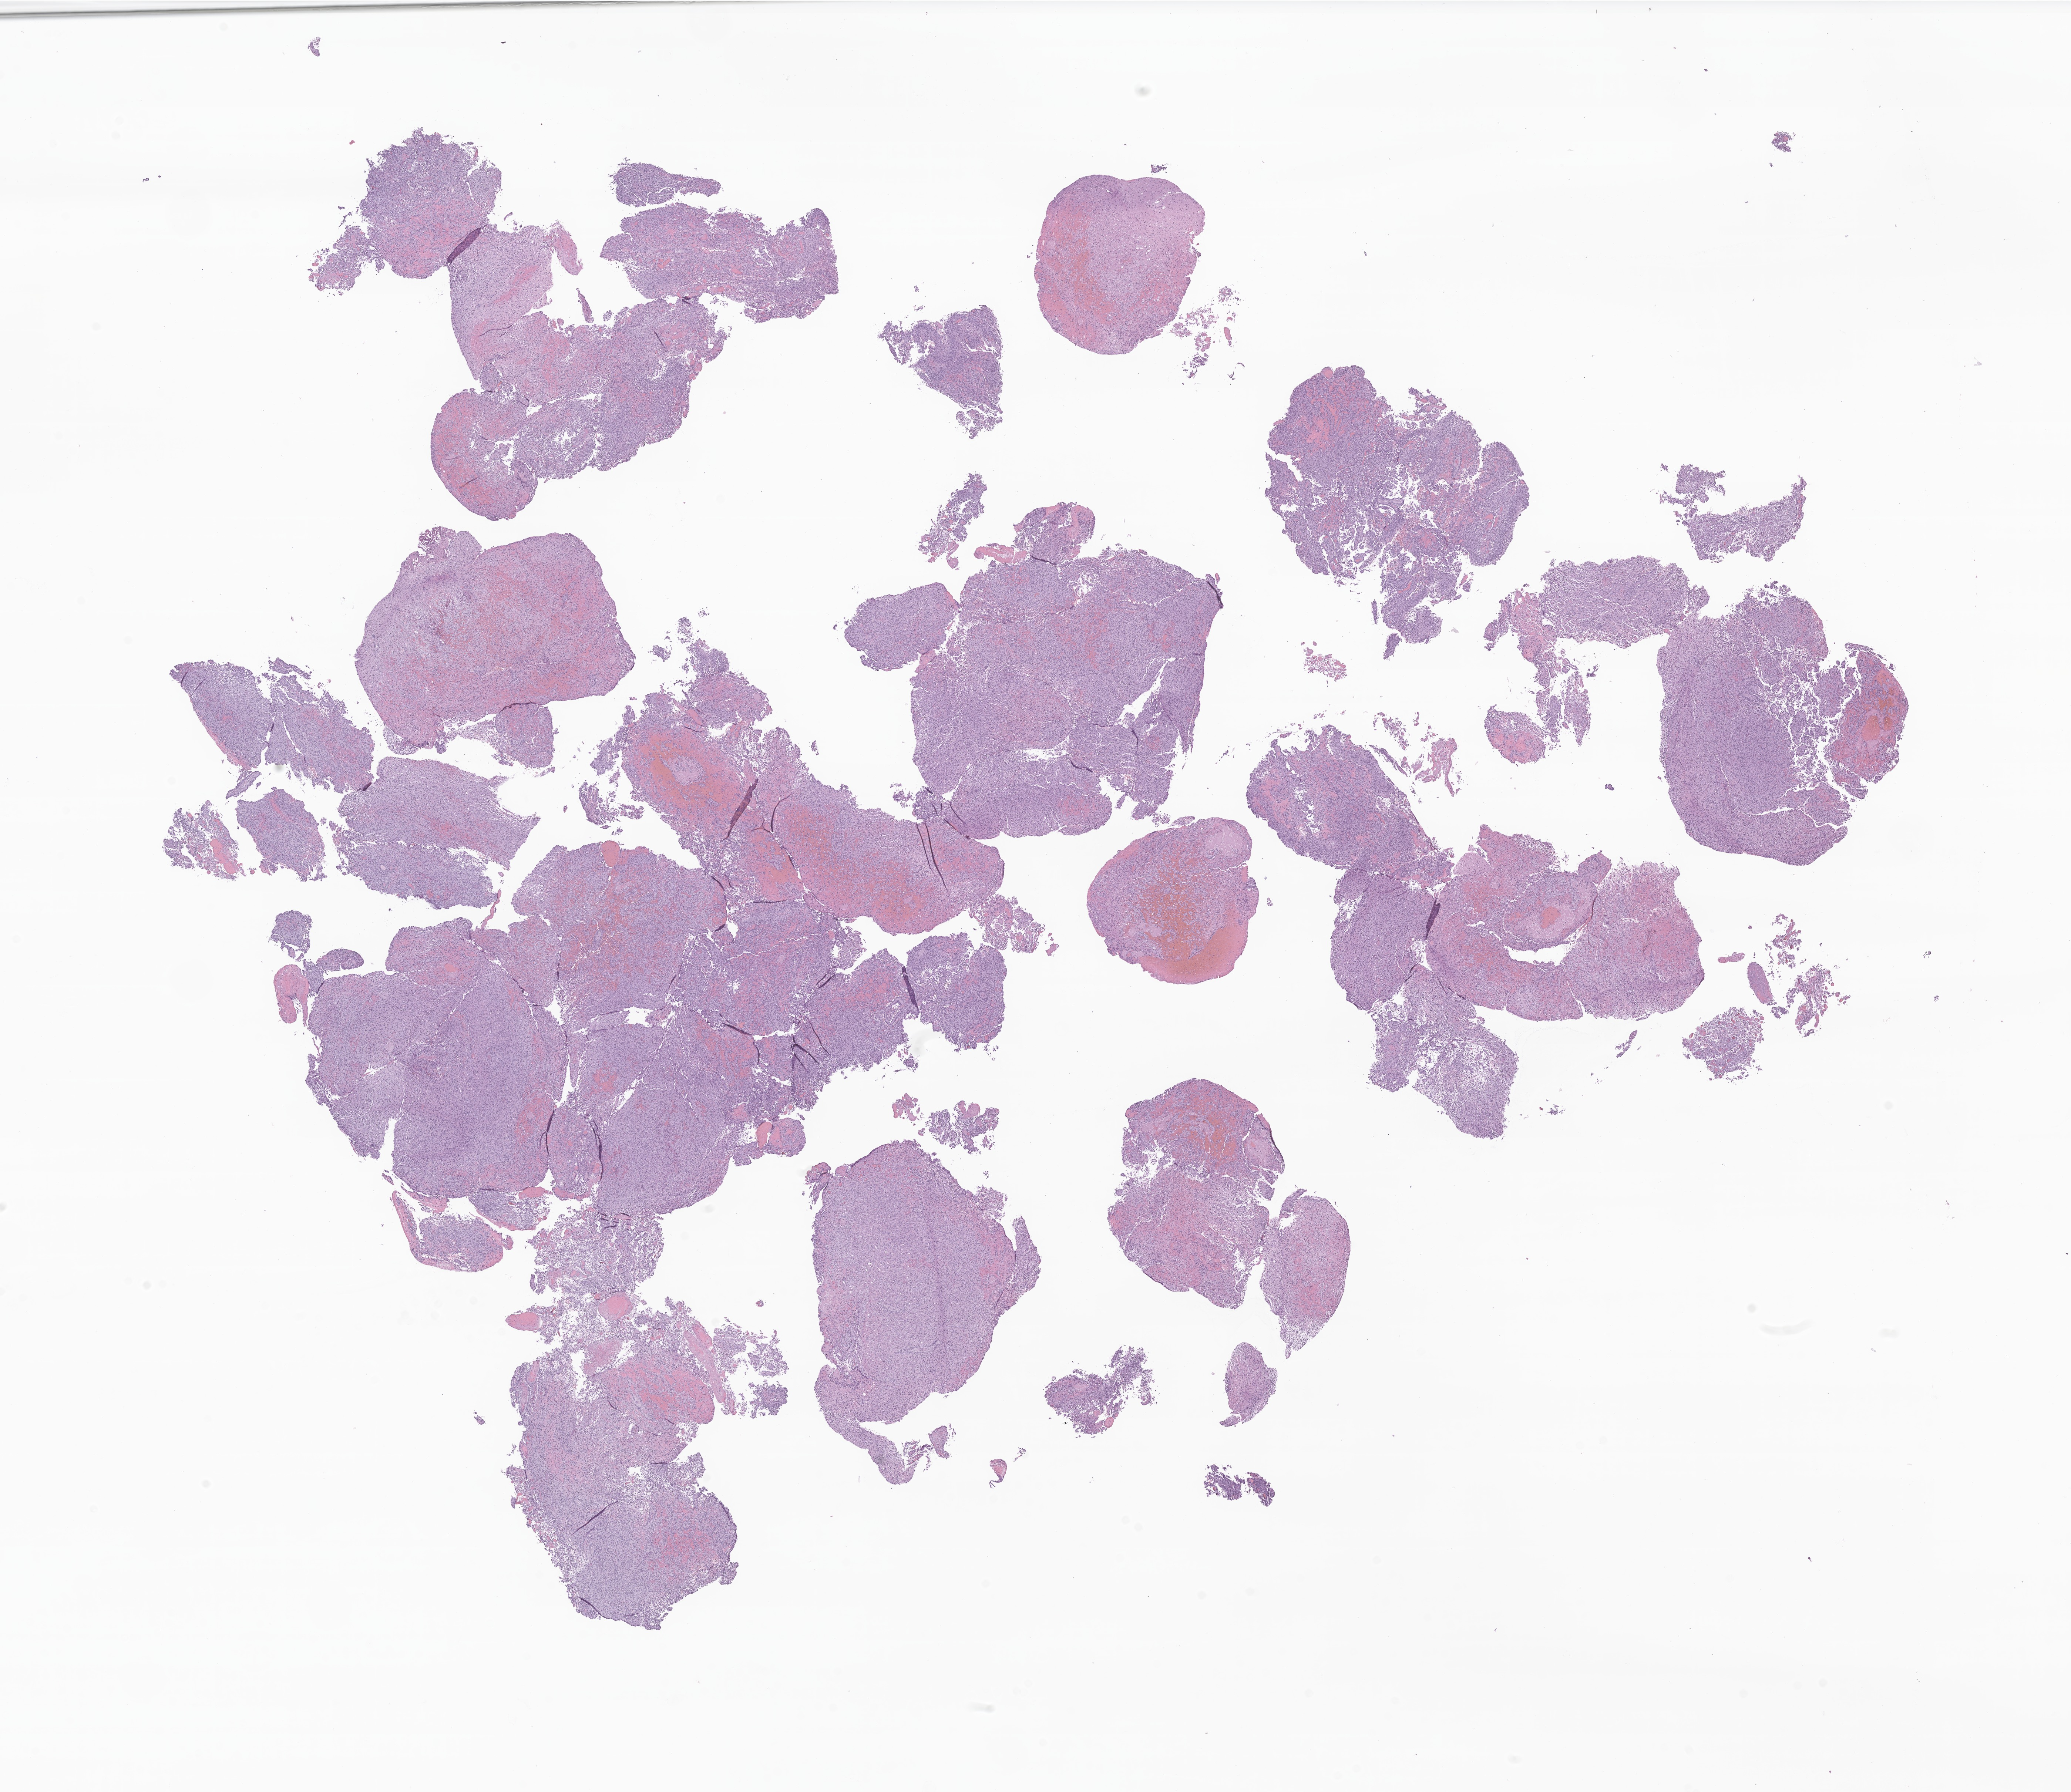
Whole-slide image, hematoxylin and eosin (H&E) stain of tumor tissue from the spinal cord — a low-resolution overview of the entire scanned area, about 23.6 x 20.4 mm, formalin-fixed, paraffin-embedded (FFPE) tissue. Female patient, age 441 days (about 1.2 years).
Recorded diagnosis: Glioma, malignant.